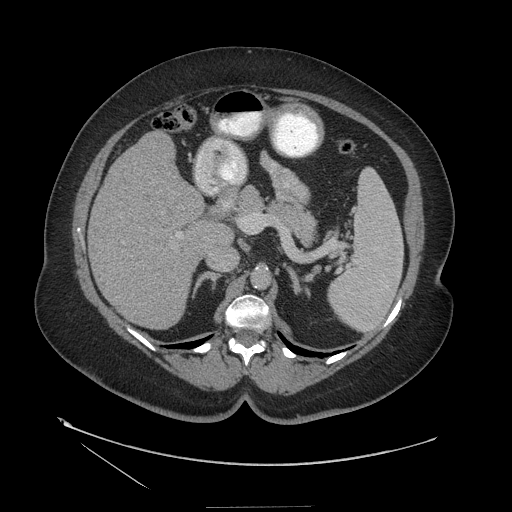
Contrast-enhanced abdominal CT (liver protocol), one axial slice. Position 68 of 127 along the scan axis. 140 kVp. Soft-tissue window (W 400 / L 40 HU). 2.5 mm slice thickness. 512 × 512 image matrix, field of view 480 × 480 mm. From the clinical record (not read from this slice): diagnosis: hepatocellular carcinoma (patient treated with transarterial chemoembolisation; whether this scan precedes or follows treatment is not stated here); TNM stage (as recorded): Stage-II; Child-Pugh class: A; tumour differentiation: well differentiated.
Annotated regions visible in this slice (semi-automatically segmented with operator editing):
- liver parenchyma outside the tumour (the mass and vessels are separate outlines, so this box may not span the whole liver): bounding box [x1, y1, x2, y2] px = [88, 132, 234, 328]